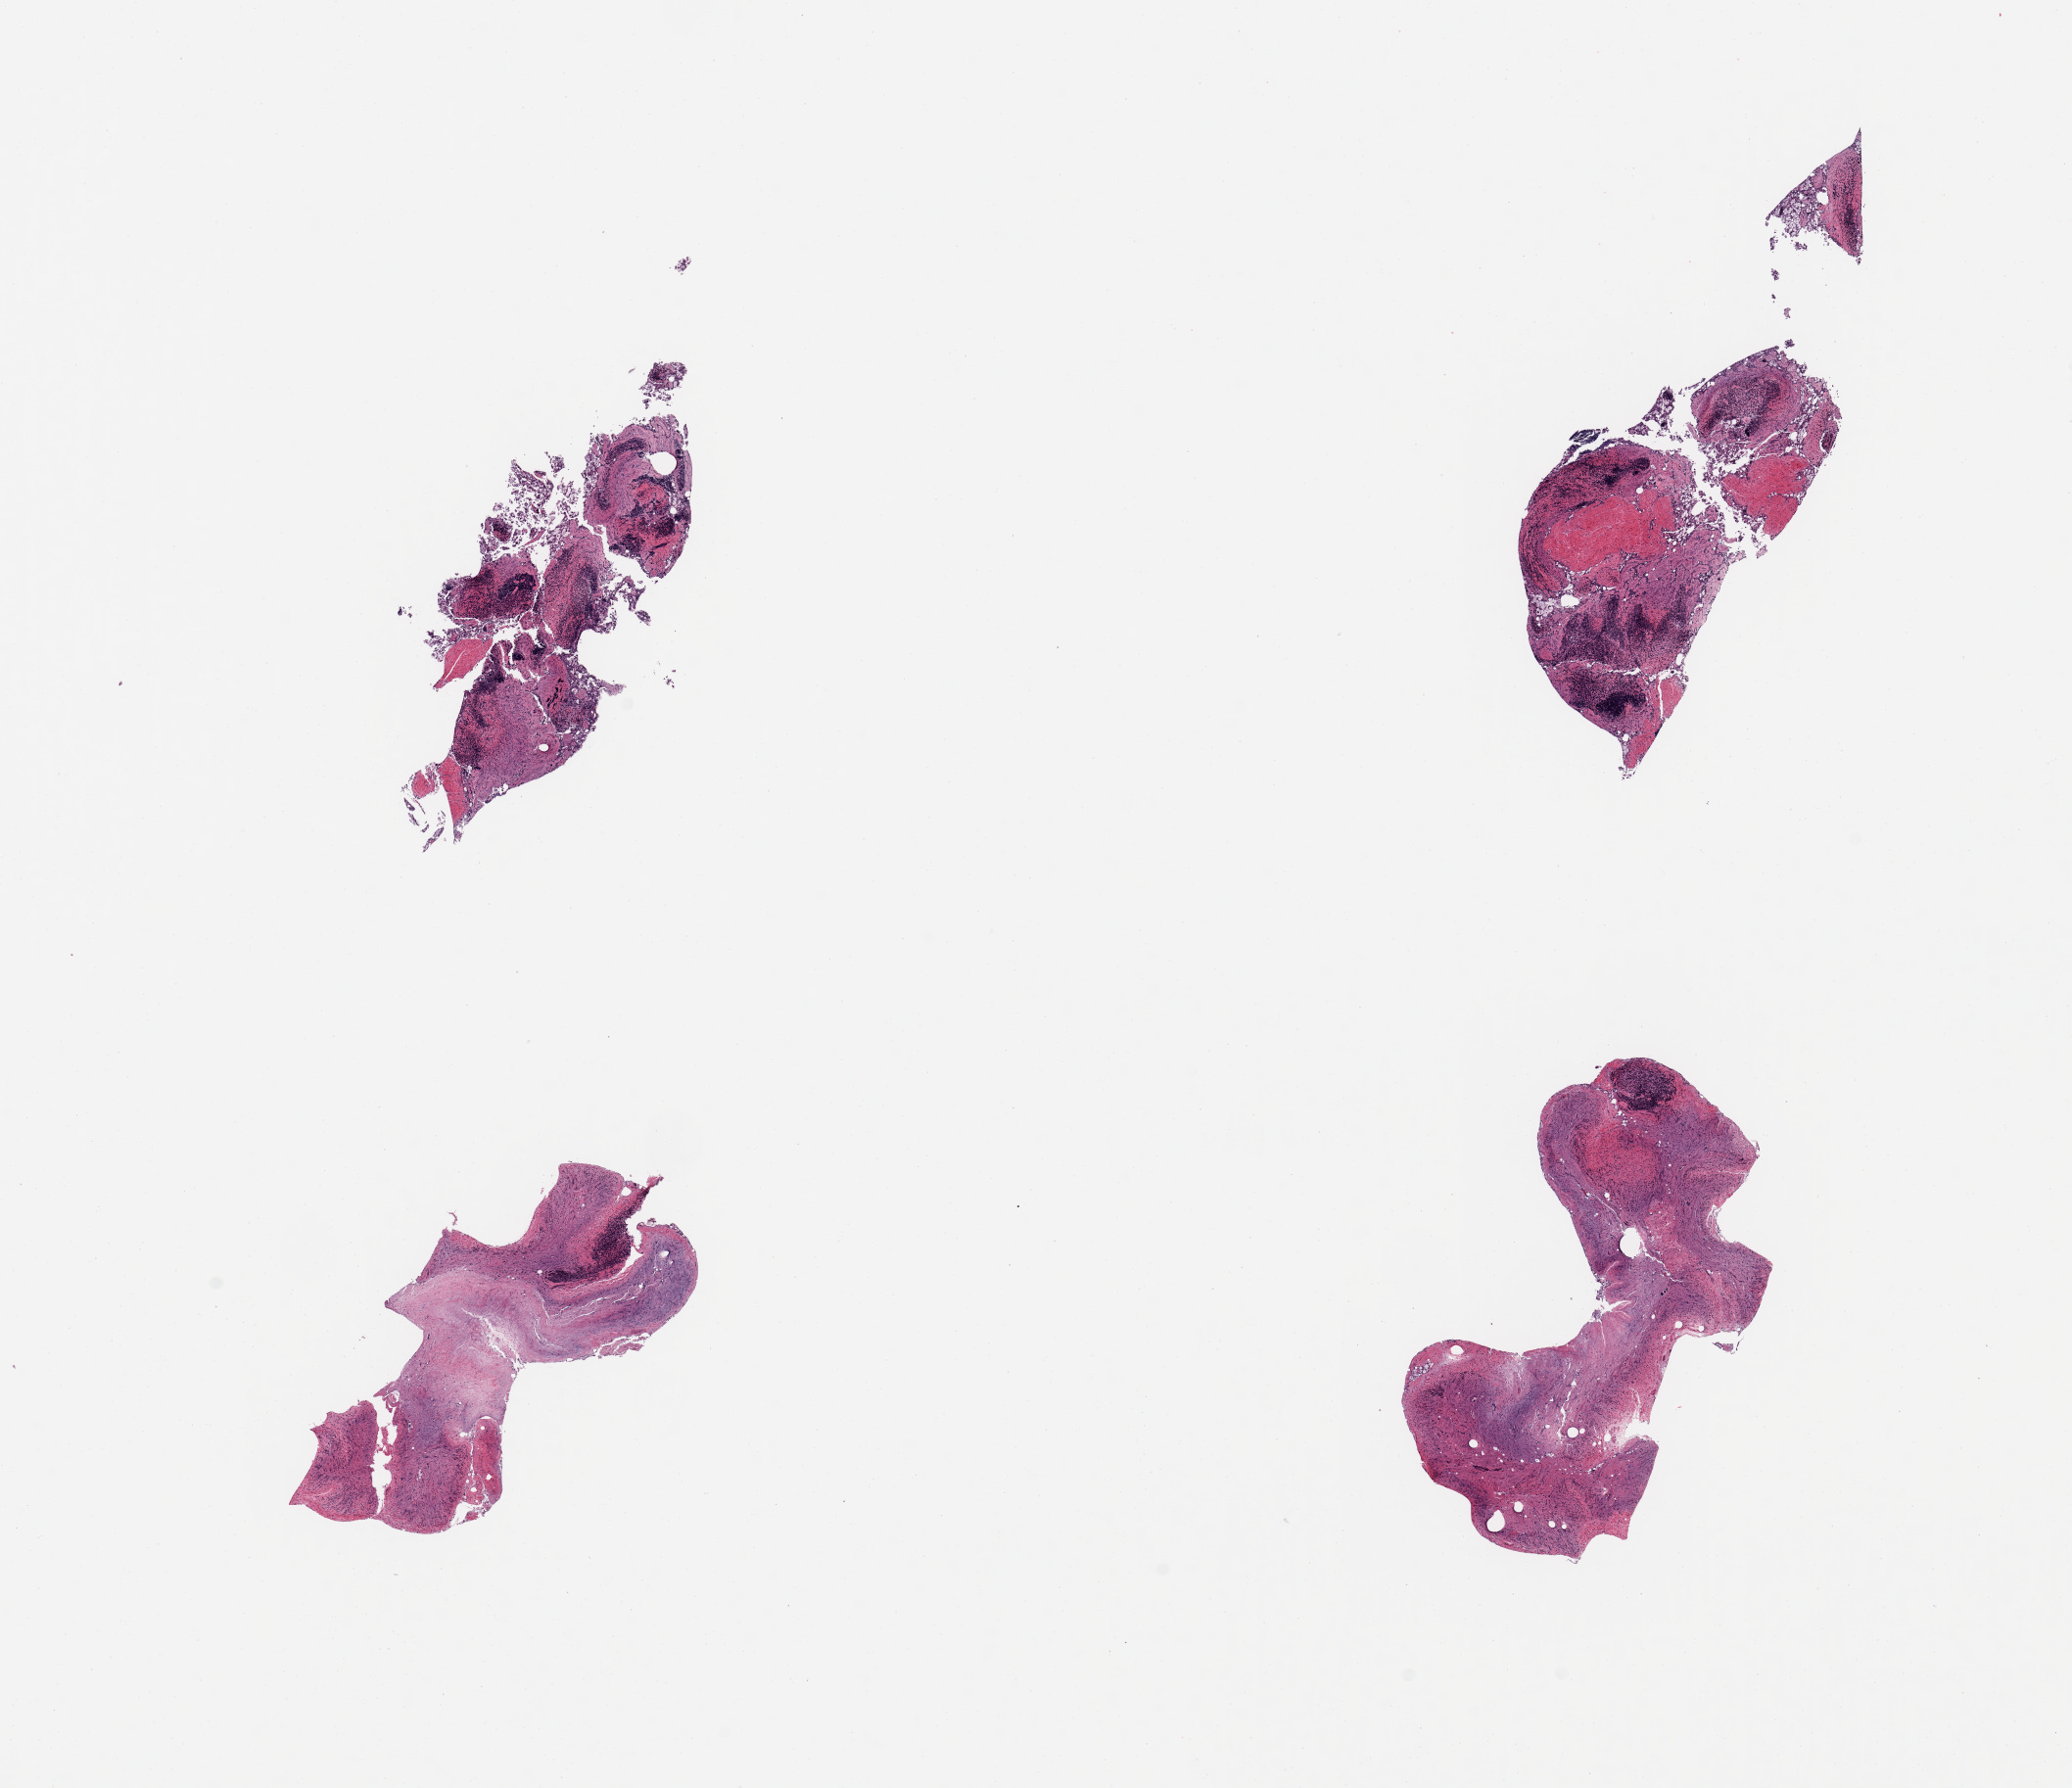
H&E whole-slide image — low-resolution overview of the scanned area, about 16.7 x 14.4 mm, PAXgene-fixed, paraffin-embedded tissue, sampled site (target tissue): ileum, tissue donor sample. Male donor.
Pathologist's review note for this sample: 4 pieces, glandular mucosa autolyzed; ~20% residual target lymhoid elements.